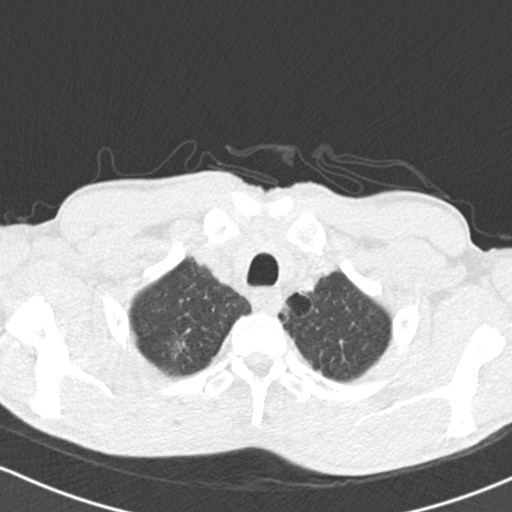
Low-dose screening chest CT, one axial slice. Slice 125 of 150 in the series (ordered by position). Reconstruction kernel B30f. Lung window (W 1500 / L -600 HU). 2 mm slice thickness. 512 × 512 image matrix, field of view 312 × 312 mm.
Structures marked on this image (outlined manually by an expert reader):
- lesion 1 (tumor, upper lobe of right lung): box from (x=175, y=342) to (x=185, y=357) px